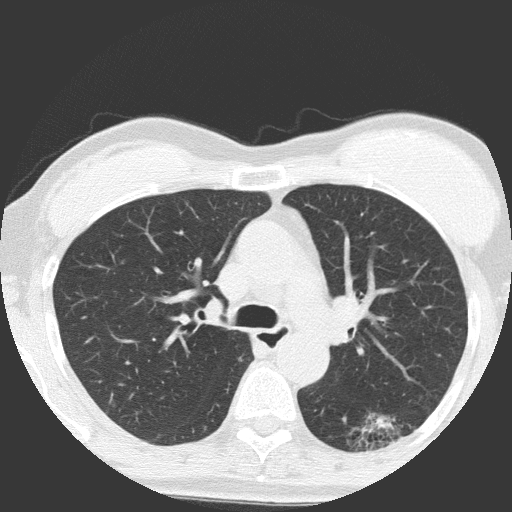
Low-dose screening chest CT, axial slice, baseline annual screen, lung window (W 1500 / L -600 HU), slice 51 of 149 in the series, 512 × 512 image matrix. Female, age 64 years at enrolment. Former smoker at enrolment.
Expert-annotated lung lesion, bounding box <334,396,422,466> (left, top, right, bottom; pixels). The exam's reader record, not a measurement of the box and not confirmed to be the same lesion: non-calcified nodule or mass ≥4 mm, right upper lobe, 4 × 4 mm, poorly defined margins, ground glass attenuation. Note: the box lies in the patient's left hemithorax on this image, whereas the reader's record names the right lung; they may be different findings. Participant outcome: lung cancer diagnosed 932 days after this screen — adenocarcinoma, NOS, left lower lobe, moderately differentiated (G2), stage IA (AJCC 6th edition), 17 mm at pathology.